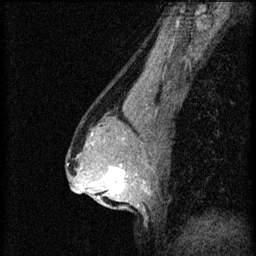
Breast MRI (dynamic contrast-enhanced), one sagittal slice. Slice 38 of 60 in the series (ordered by position). 3 images stored at this slice position (order not interpretable as contrast timing). 1.5 T. TE 4.2 ms, TR 8.2 ms. 2 mm slice thickness. 256 × 256 image matrix, field of view 180 × 180 mm. Patient: female, 44 years.
Outlined on this slice (semi-automatic segmentation, software-assisted and operator-edited):
- analysis volume of interest (the breast-tissue region the enhancement analysis was run in; not a lesion): bounding box [x1, y1, x2, y2] px = [94, 162, 143, 205]
- tumour enhancement mask (voxels above the 70 % enhancement threshold inside the analysis volume of interest): [98, 164, 125, 199]